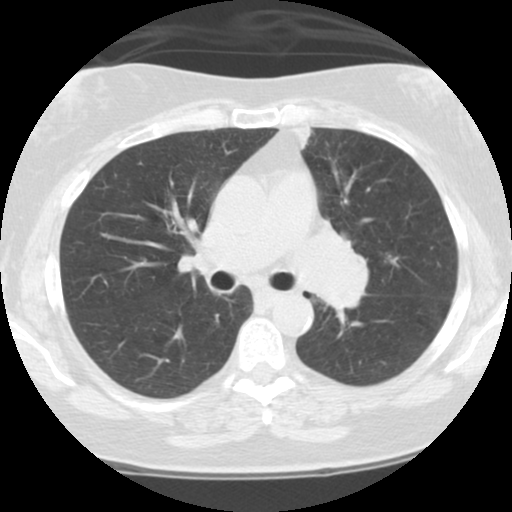
Chest CT (low-dose screening protocol), one axial image. Third annual screen. Lung window (W 1500 / L -600 HU). 2.5 mm slice thickness. Slice 42 of 108 in the series. 512 × 512 image matrix. Female participant, aged 59 years at enrolment. Current smoker at enrolment.
Expert reader's lesion annotation, box from (x=285, y=213) to (x=385, y=325) px. Screening reader's record for this exam: no non-calcified nodule ≥4 mm recorded. Lung cancer was diagnosed 192 days after this screen: small cell carcinoma, NOS, left upper lobe, left hilum, mediastinum, left main stem bronchus, stage IV (AJCC 6th edition), 63 mm at pathology.